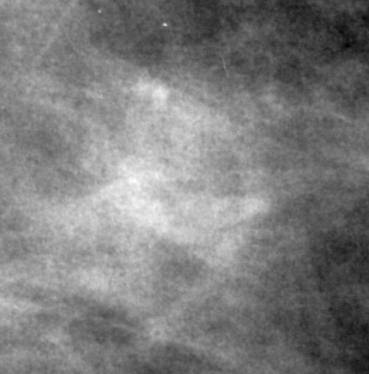
Region of interest cut from a scanned film mammogram (one marked finding), right breast, MLO view.
Mass, shape irregular, margins ill defined; BI-RADS assessment category 4; pathology result (as recorded, not read from the image): benign.